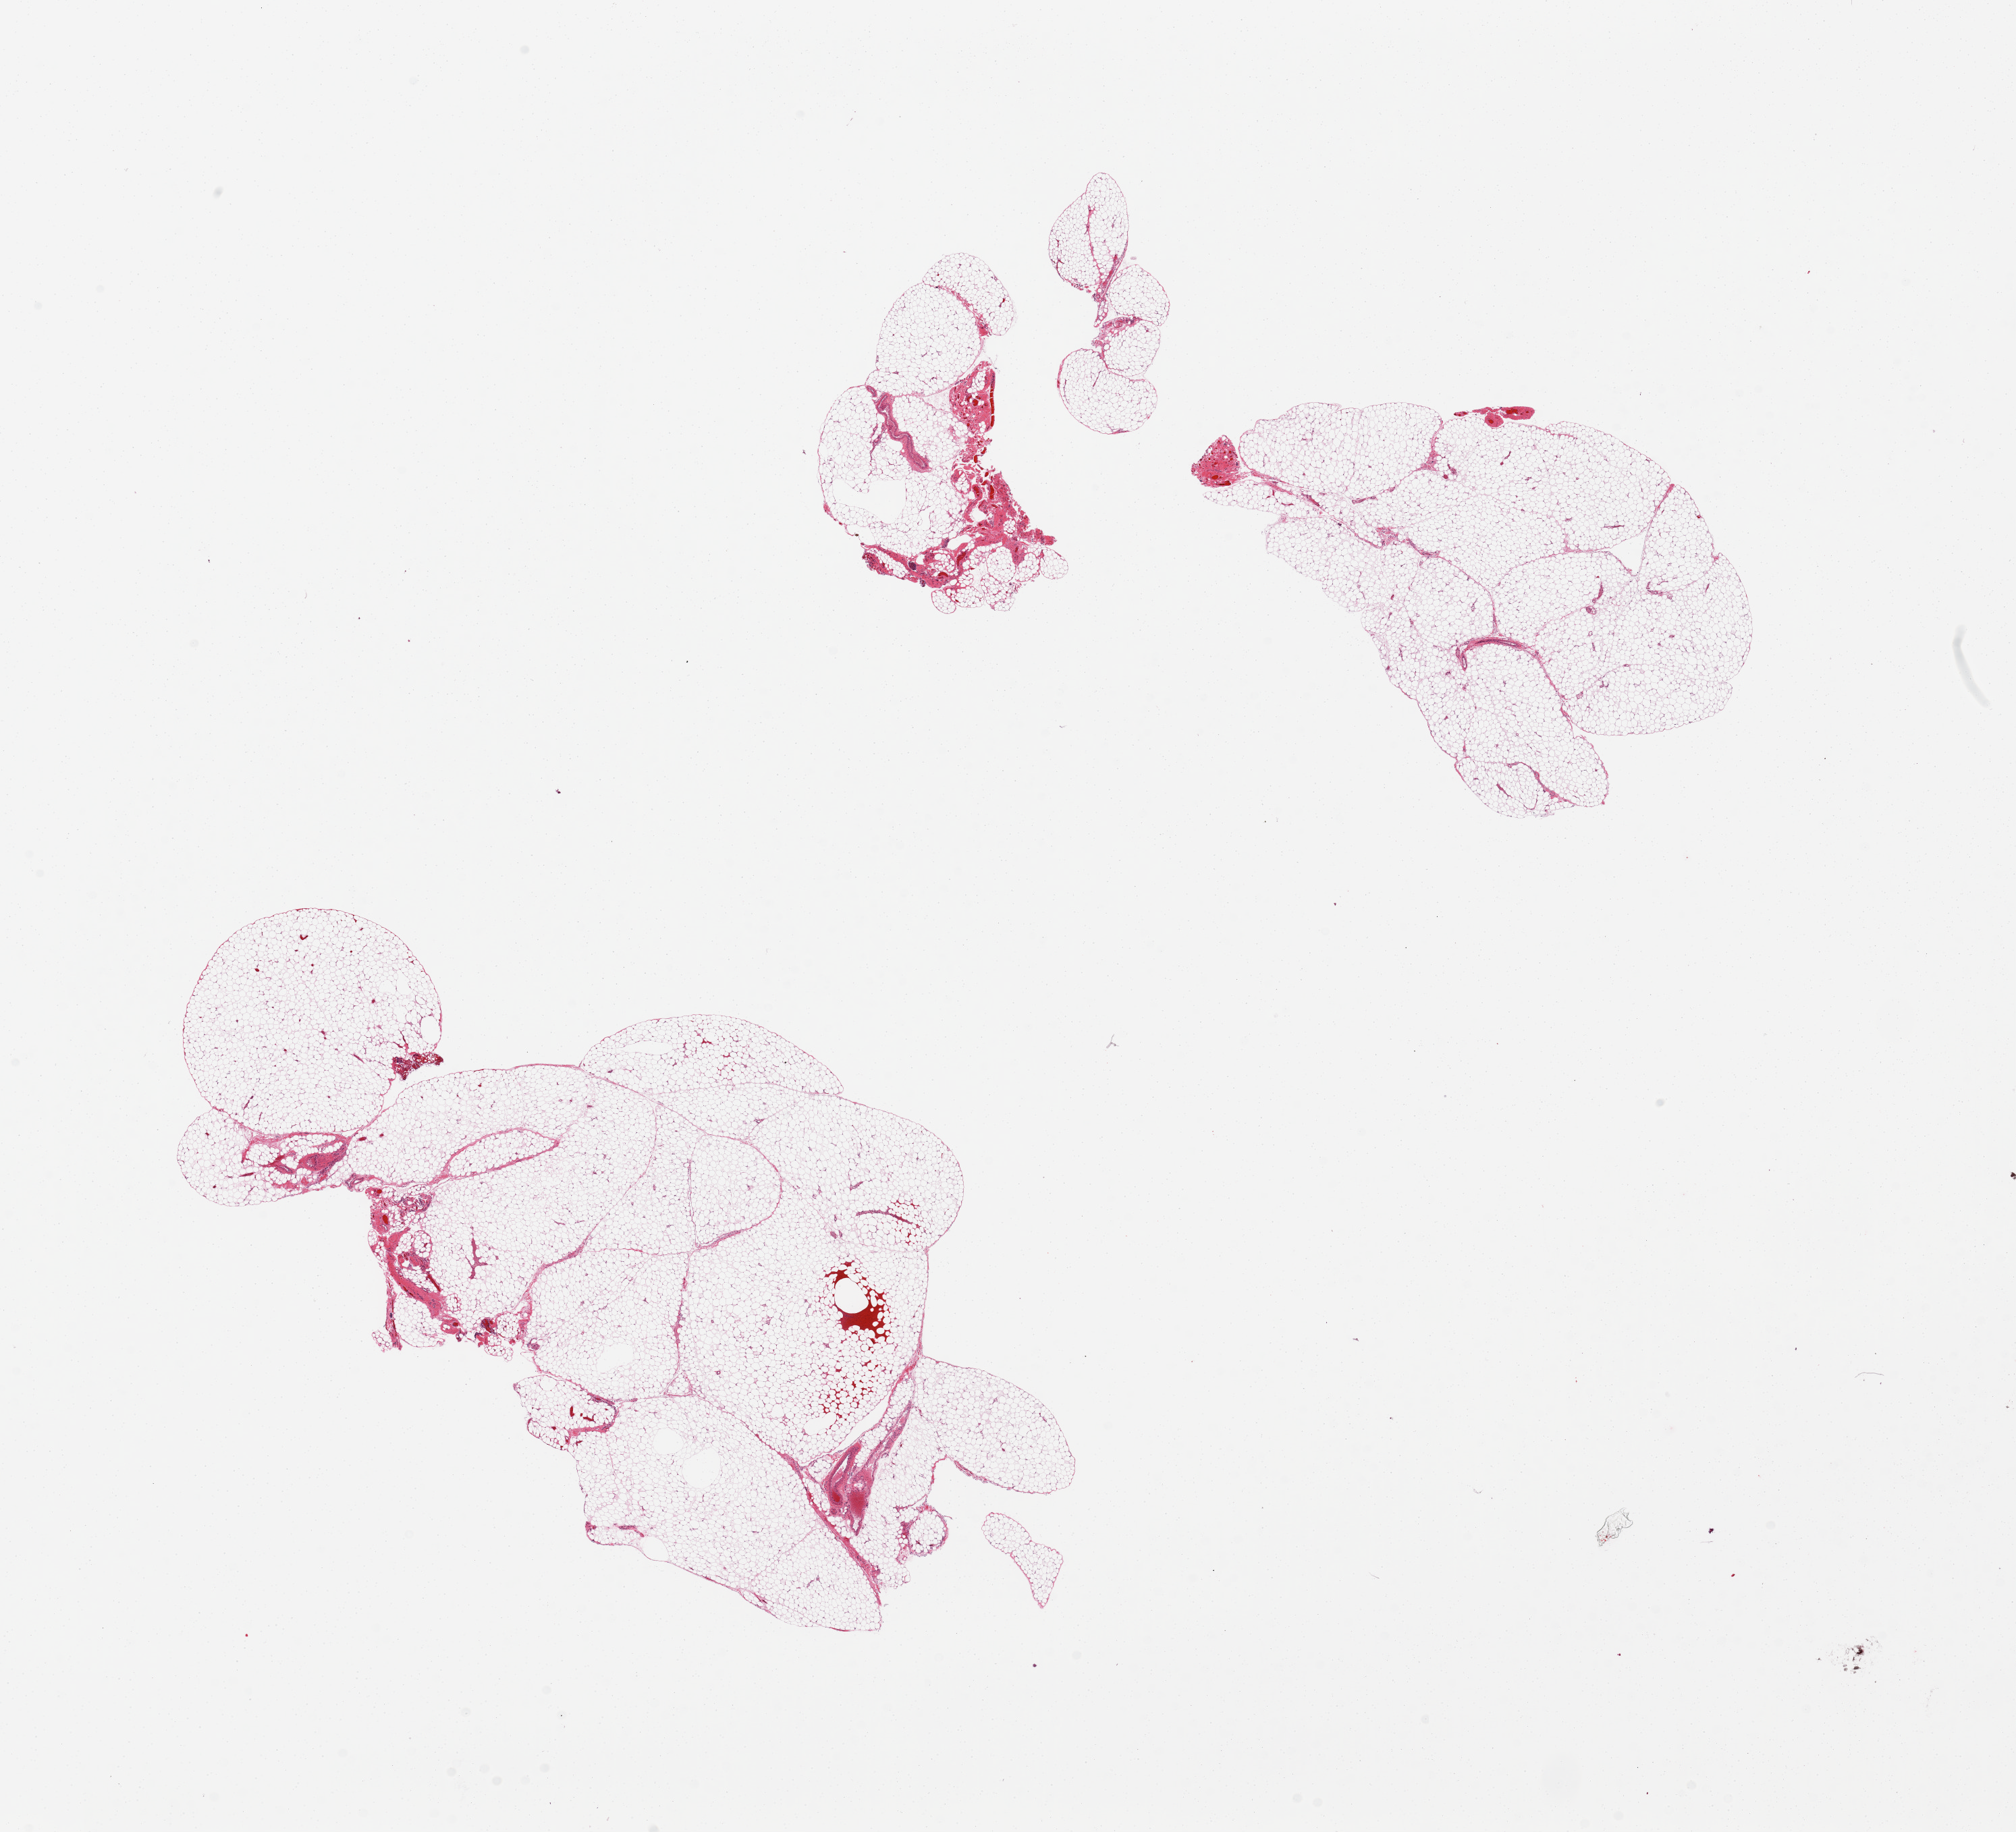
Hematoxylin and eosin (H&E) whole-slide image — a low-resolution overview of the entire scanned area, about 23.6 x 21.5 mm, PAXgene-fixed, paraffin-embedded tissue, section of omentum (target tissue), tissue donor sample. Donor sex: male.
Review note (as recorded): 2 pieces.